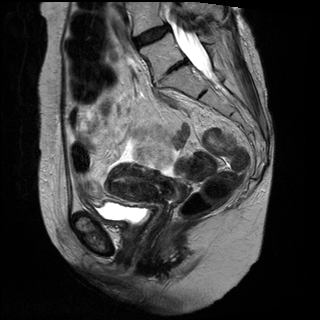
Pelvic MRI for cervical cancer, one sagittal slice; slice 15 of 31 in the series (ordered by position); T2-weighted; 1.5 T; TE 89 ms, TR 3890 ms; 4 mm slice thickness; 320 × 320 image matrix, field of view 260 × 260 mm. Female patient, age 61 years.
Structures marked on this image (manually delineated by an expert):
- uterus and cervix: bounding box (x1, y1, x2, y2) in pixels: (105, 162, 190, 207)